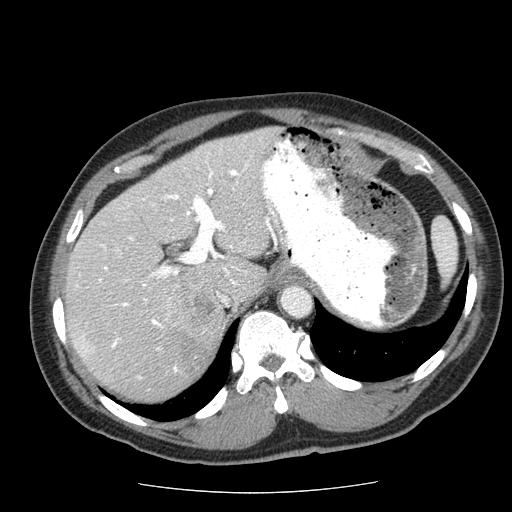
Contrast-enhanced abdominal CT (liver protocol), one axial slice. Slice 43 of 85 in the series (ordered by position). Reconstruction kernel STANDARD. Soft-tissue window (W 400 / L 40 HU). 2.5 mm slice thickness. 512 × 512 image matrix. Case-level facts recorded for this patient, not image findings: diagnosis: hepatocellular carcinoma (patient treated with transarterial chemoembolisation; whether this scan precedes or follows treatment is not stated here); TNM stage (as recorded): Stage-IIIA; Child-Pugh class: A; tumour nodularity: multinodular; tumour size: 8 cm.
Structures marked on this image (semi-automatically segmented with operator editing):
- liver parenchyma outside the tumour (the mass and vessels are separate outlines, so this box may not span the whole liver): bounding box (x1, y1, x2, y2) in pixels: (64, 128, 279, 400)
- mass: (166, 286, 223, 370)
- liver vessels: (75, 156, 270, 379)